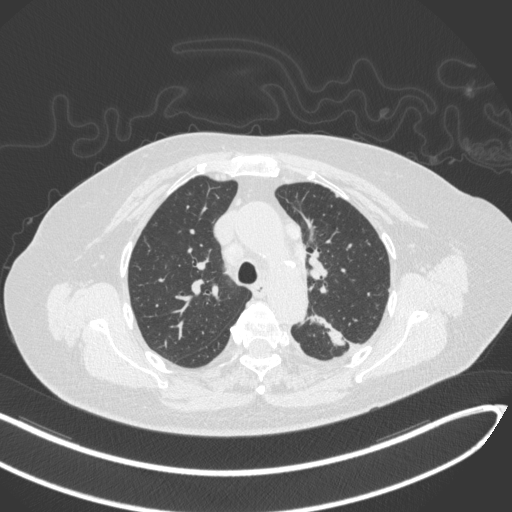
Chest CT, one axial slice. Position 223 of 270 along the scan axis. Reconstruction kernel B31f. Lung window (W 1500 / L -600 HU). 512 × 512 image matrix, field of view 400 × 400 mm. Female patient, age 76 years. Case-level facts recorded for this patient, not image findings: clinical TNM (as recorded): T1c N0 M0.
Outlined on this slice (bounding box drawn by a radiologist):
- lung tumour (recorded histology: adenocarcinoma): bounding box (x1, y1, x2, y2) in pixels: (311, 306, 351, 351)